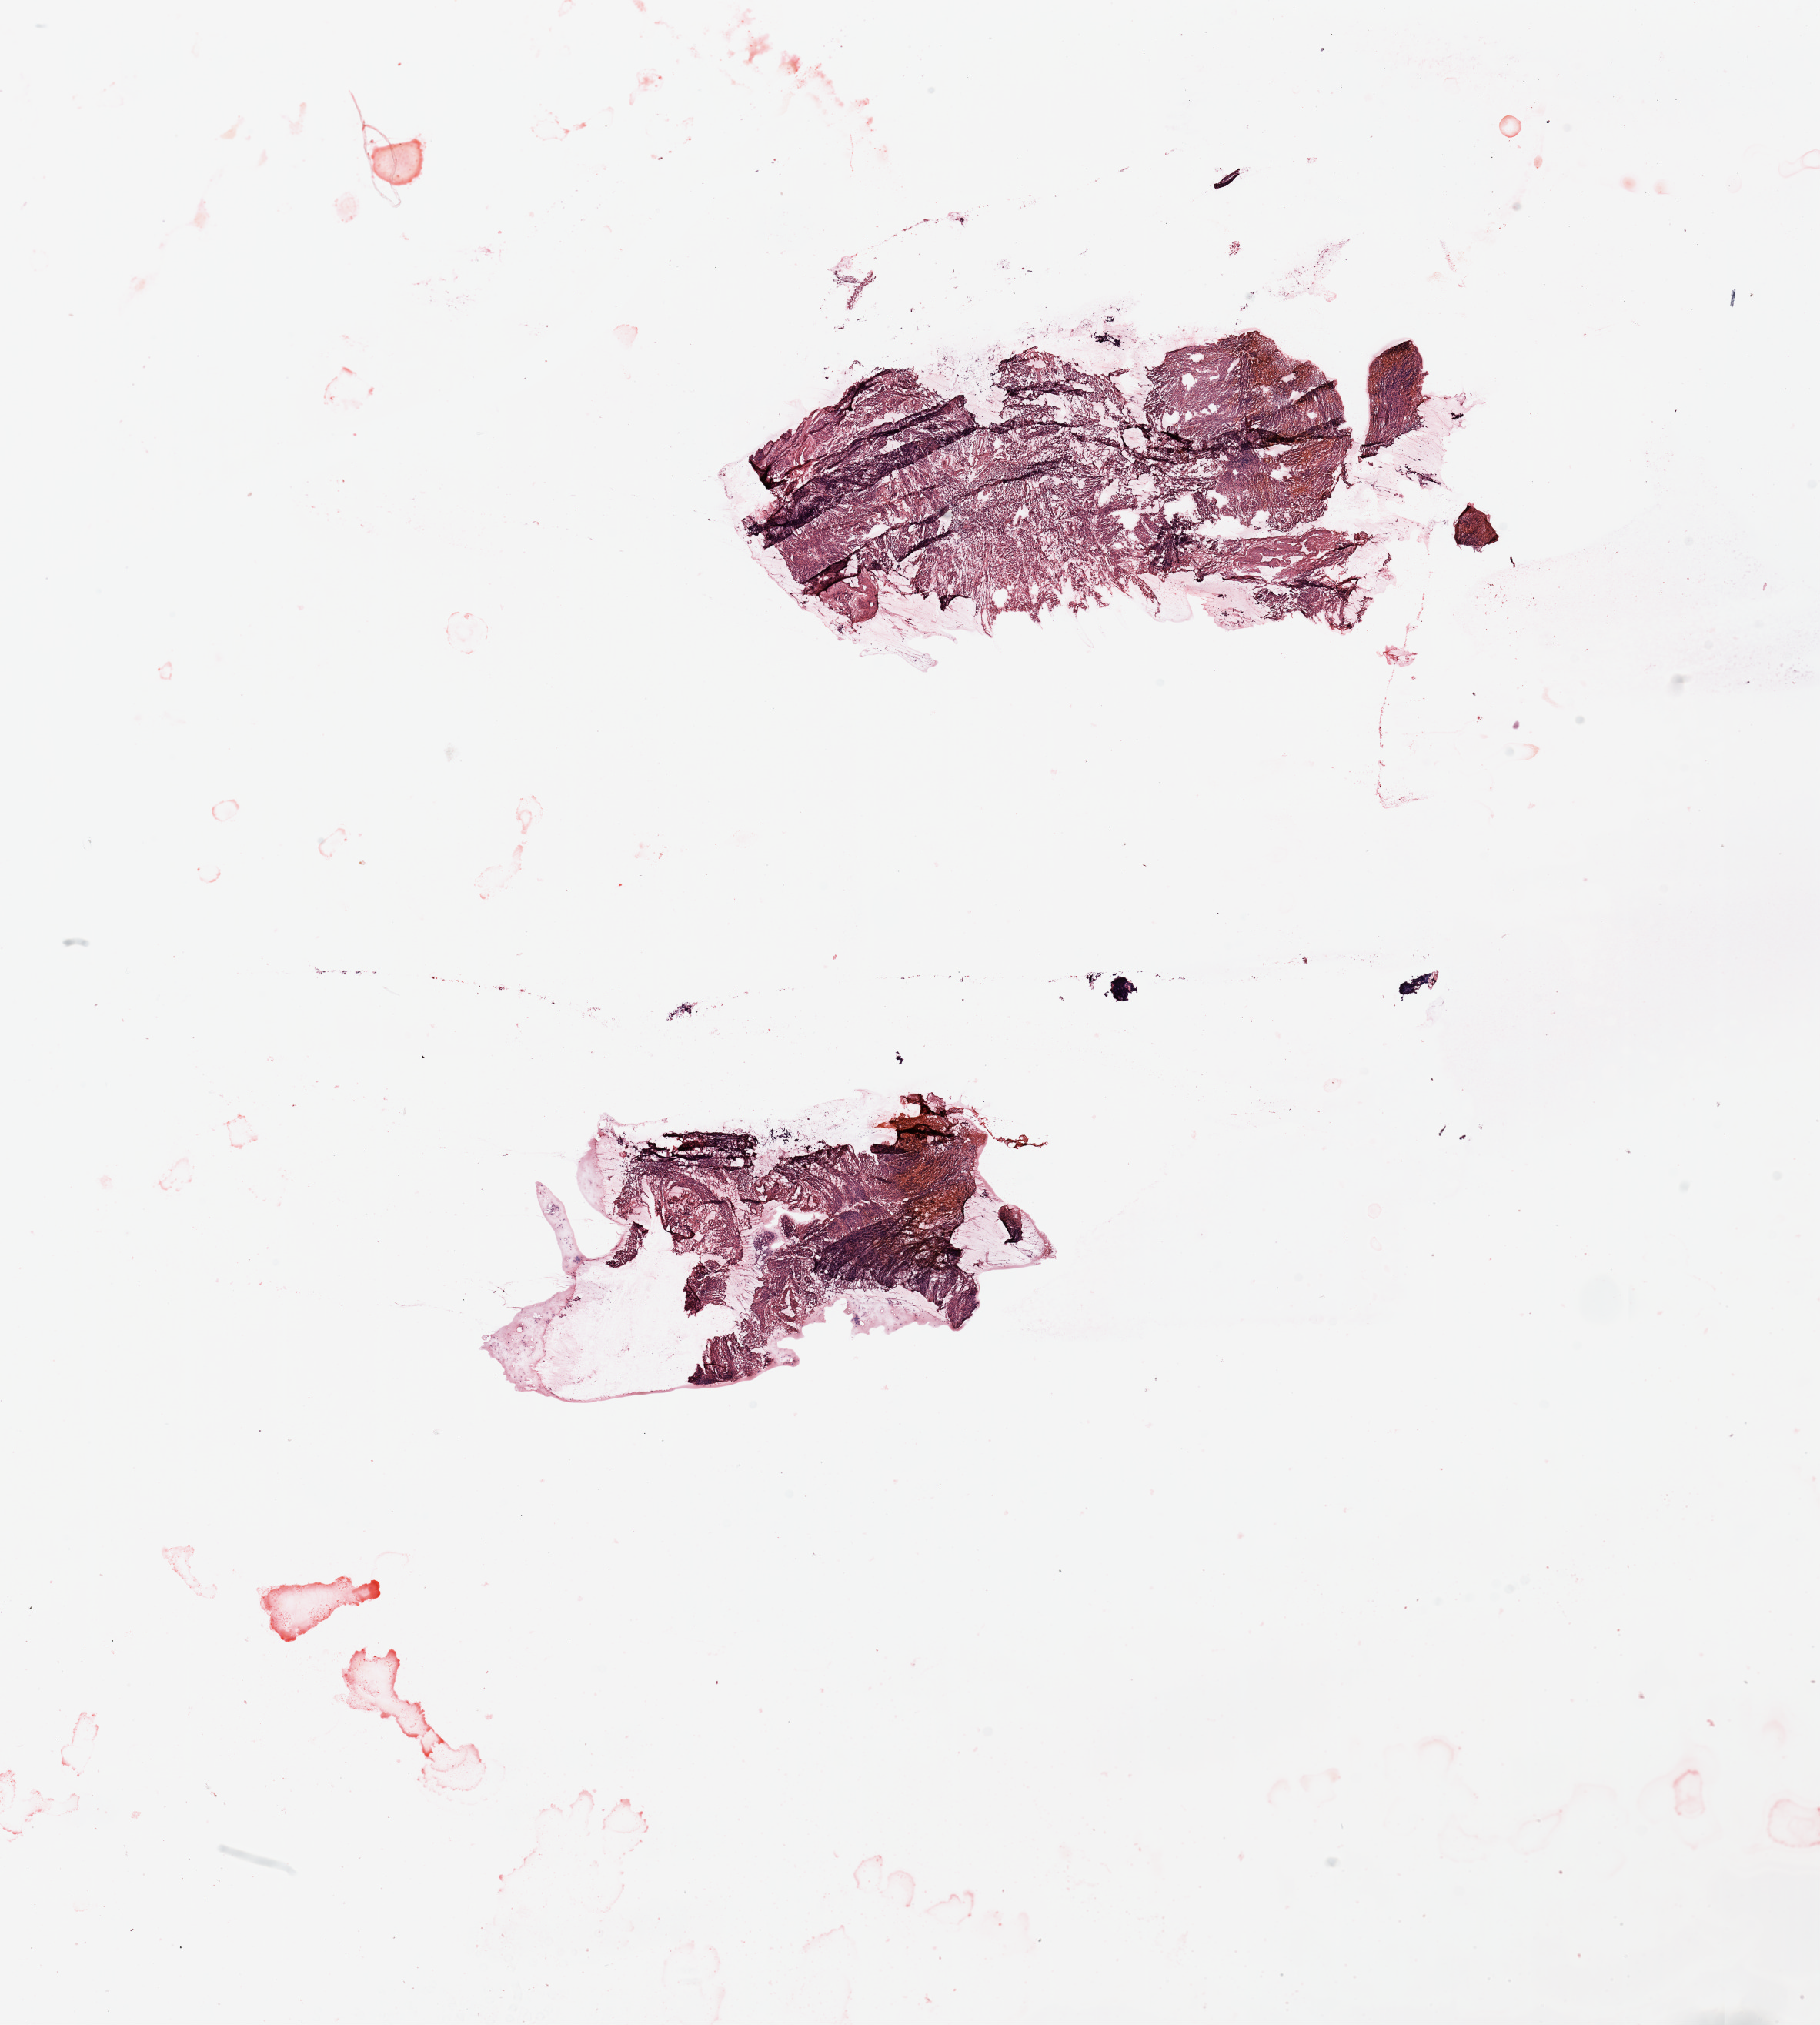
Digitized Hematoxylin and eosin (H&E) stained tissue section (whole slide), a low-resolution overview of the entire scanned area, about 18.7 x 20.8 mm (from a 20x scan). Normal (non-tumour) tissue sample, uterus. Patient: female, age 67 years.
This section: normal (non-tumour) tissue from the same patient. Patient diagnosis: Endometrioid adenocarcinoma, NOS.